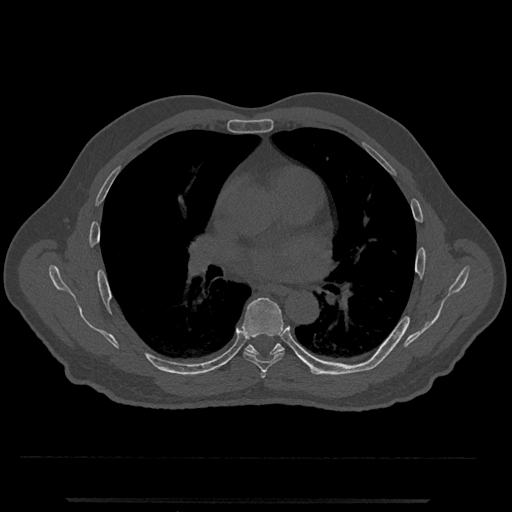
CT including the spine, one axial slice. Bone window (W 1800 / L 400 HU). 0.5 mm slice thickness. 512 × 512 image matrix, field of view 419 × 419 mm. Male patient, age 63 years. Case-level facts recorded for this patient, not image findings: primary cancer: prostate.
Structures marked on this image (semi-automatically segmented with operator editing):
- T5 vertebra: bounding box (x1, y1, x2, y2) in pixels: (260, 371, 267, 379)
- T6 vertebra: (242, 297, 284, 372)
- T7 vertebra: (245, 343, 320, 375)